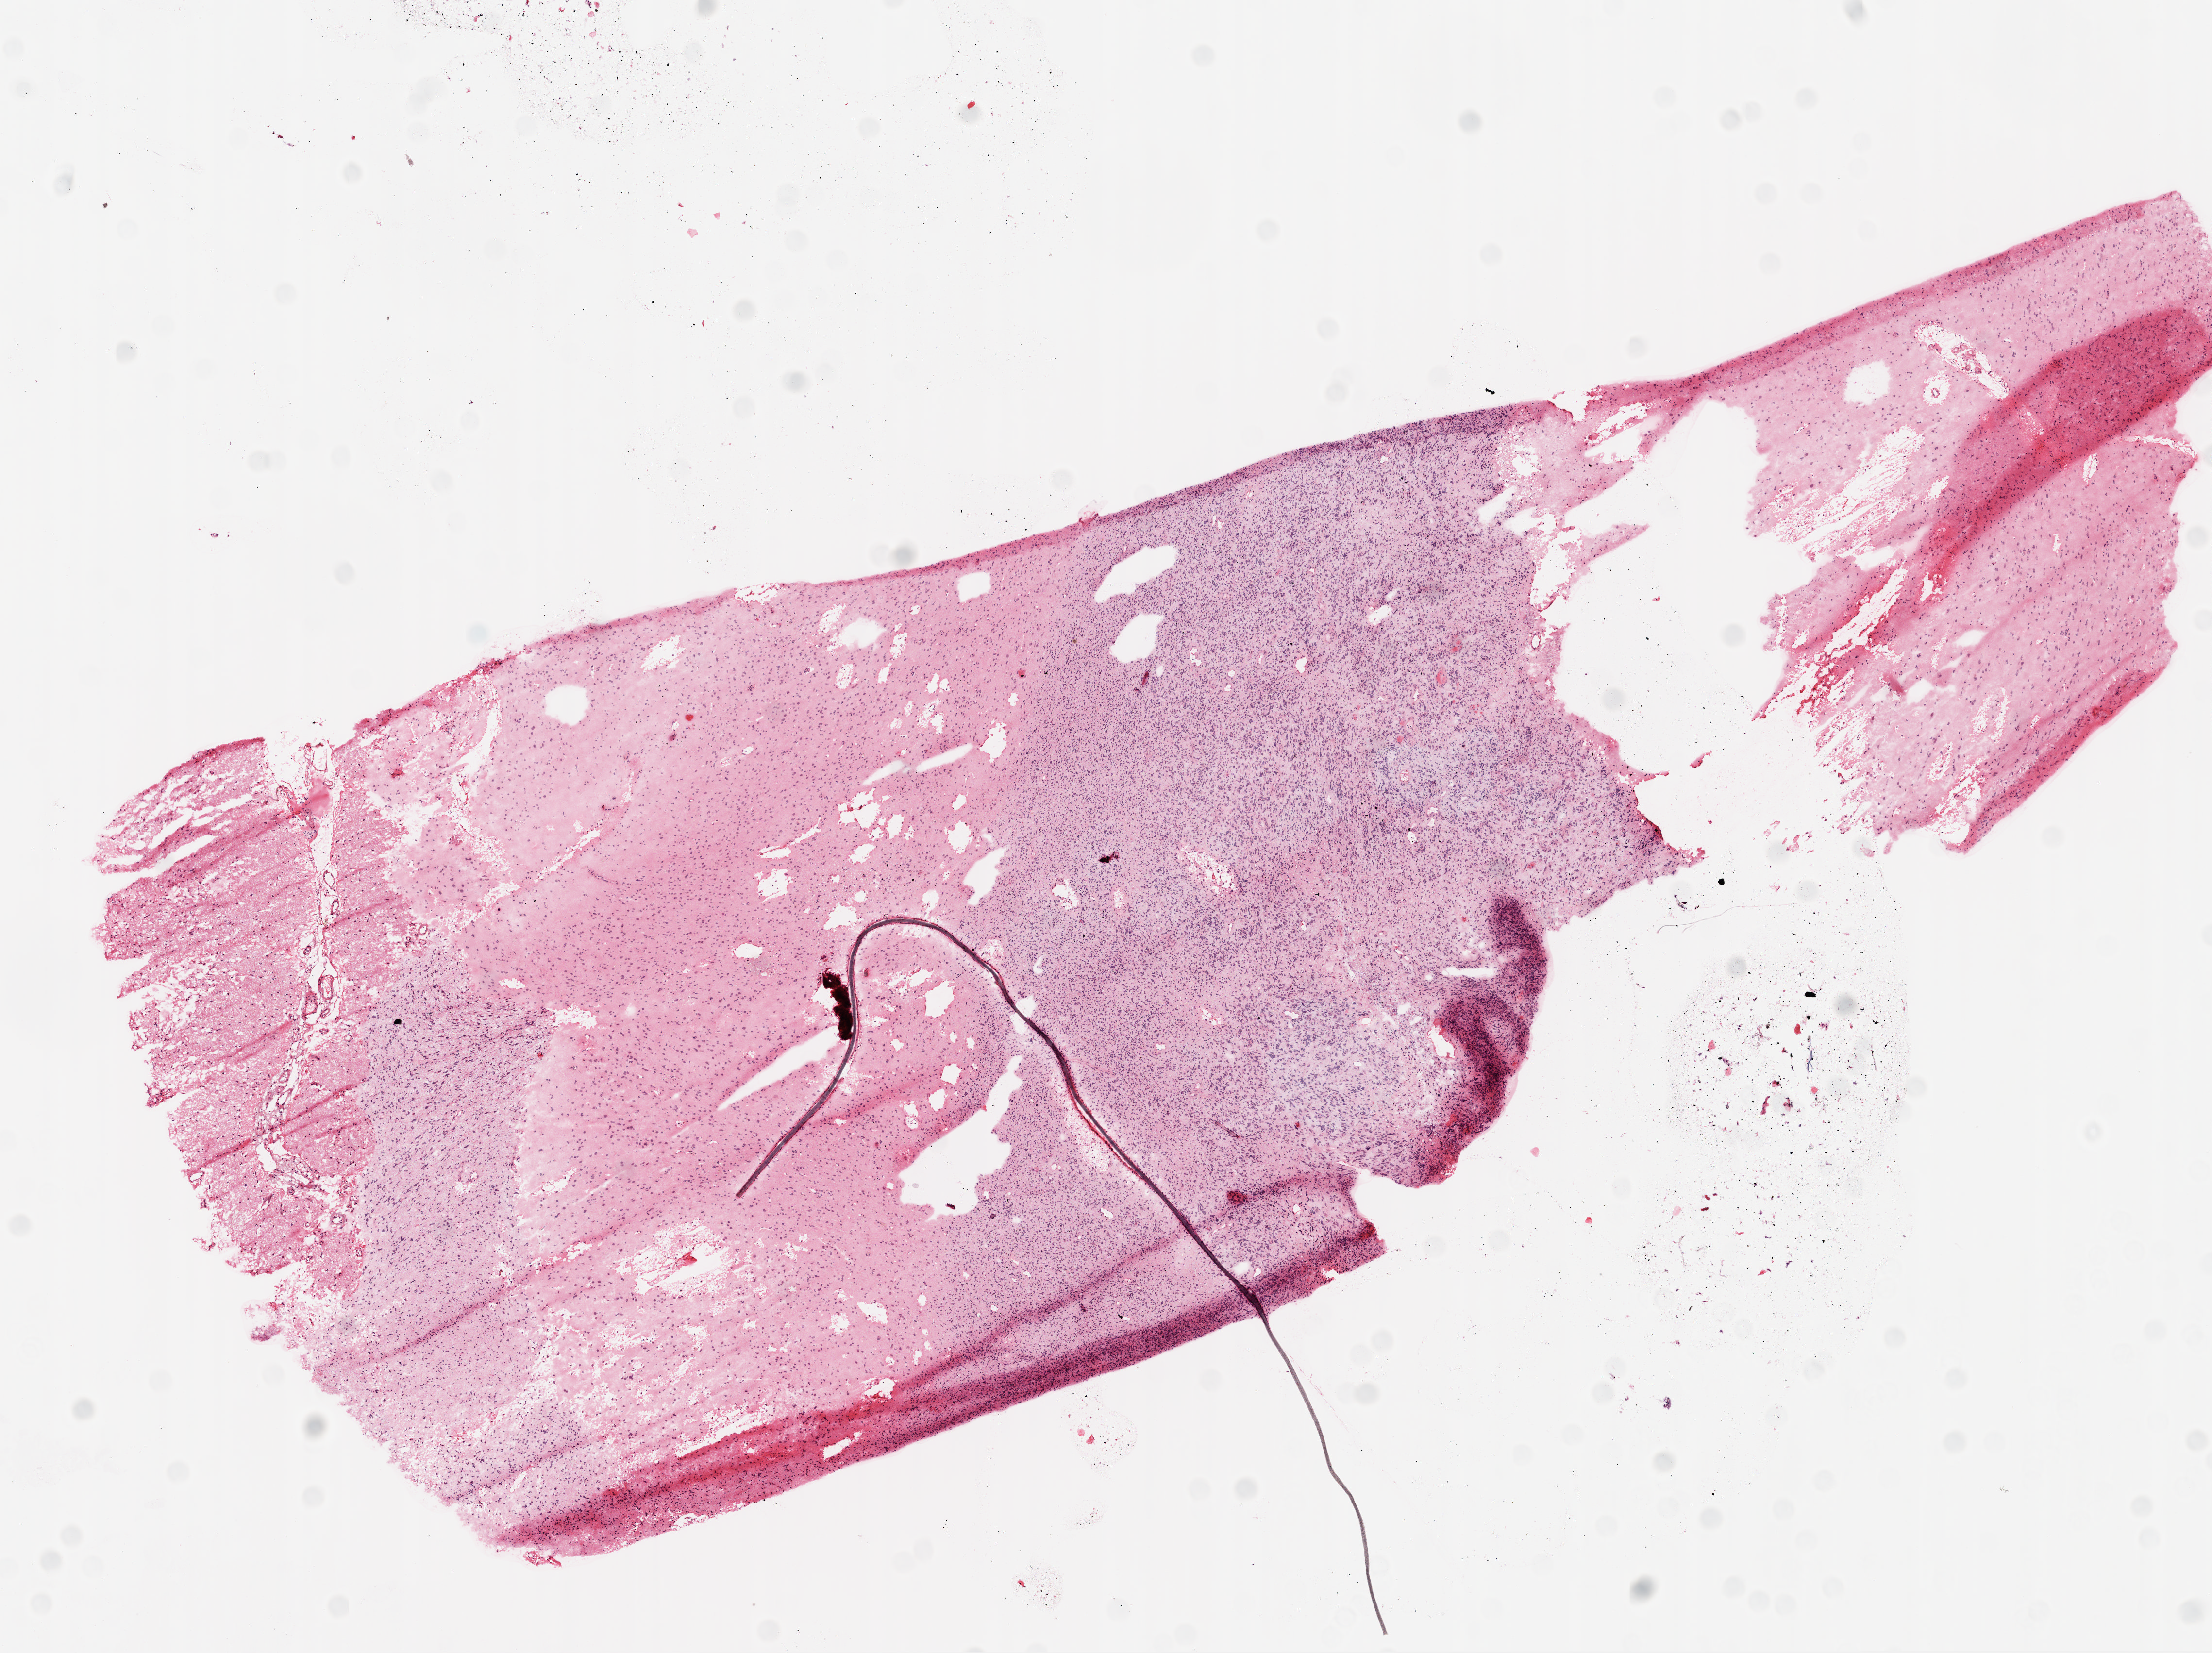
Digitized H&E tissue section (whole slide), low-resolution overview of the scanned area, about 9.2 x 6.9 mm (from a 20x scan). Frozen section from the bottom of the tissue portion. Brain, primary tumour sample. Female, age 59 years at initial diagnosis. Slide review estimates, as recorded: tumour cells 35%, tumour nuclei 85%, normal cells 5%, stromal cells 55%, necrosis 5%.
Pathologic diagnosis: Glioblastoma.